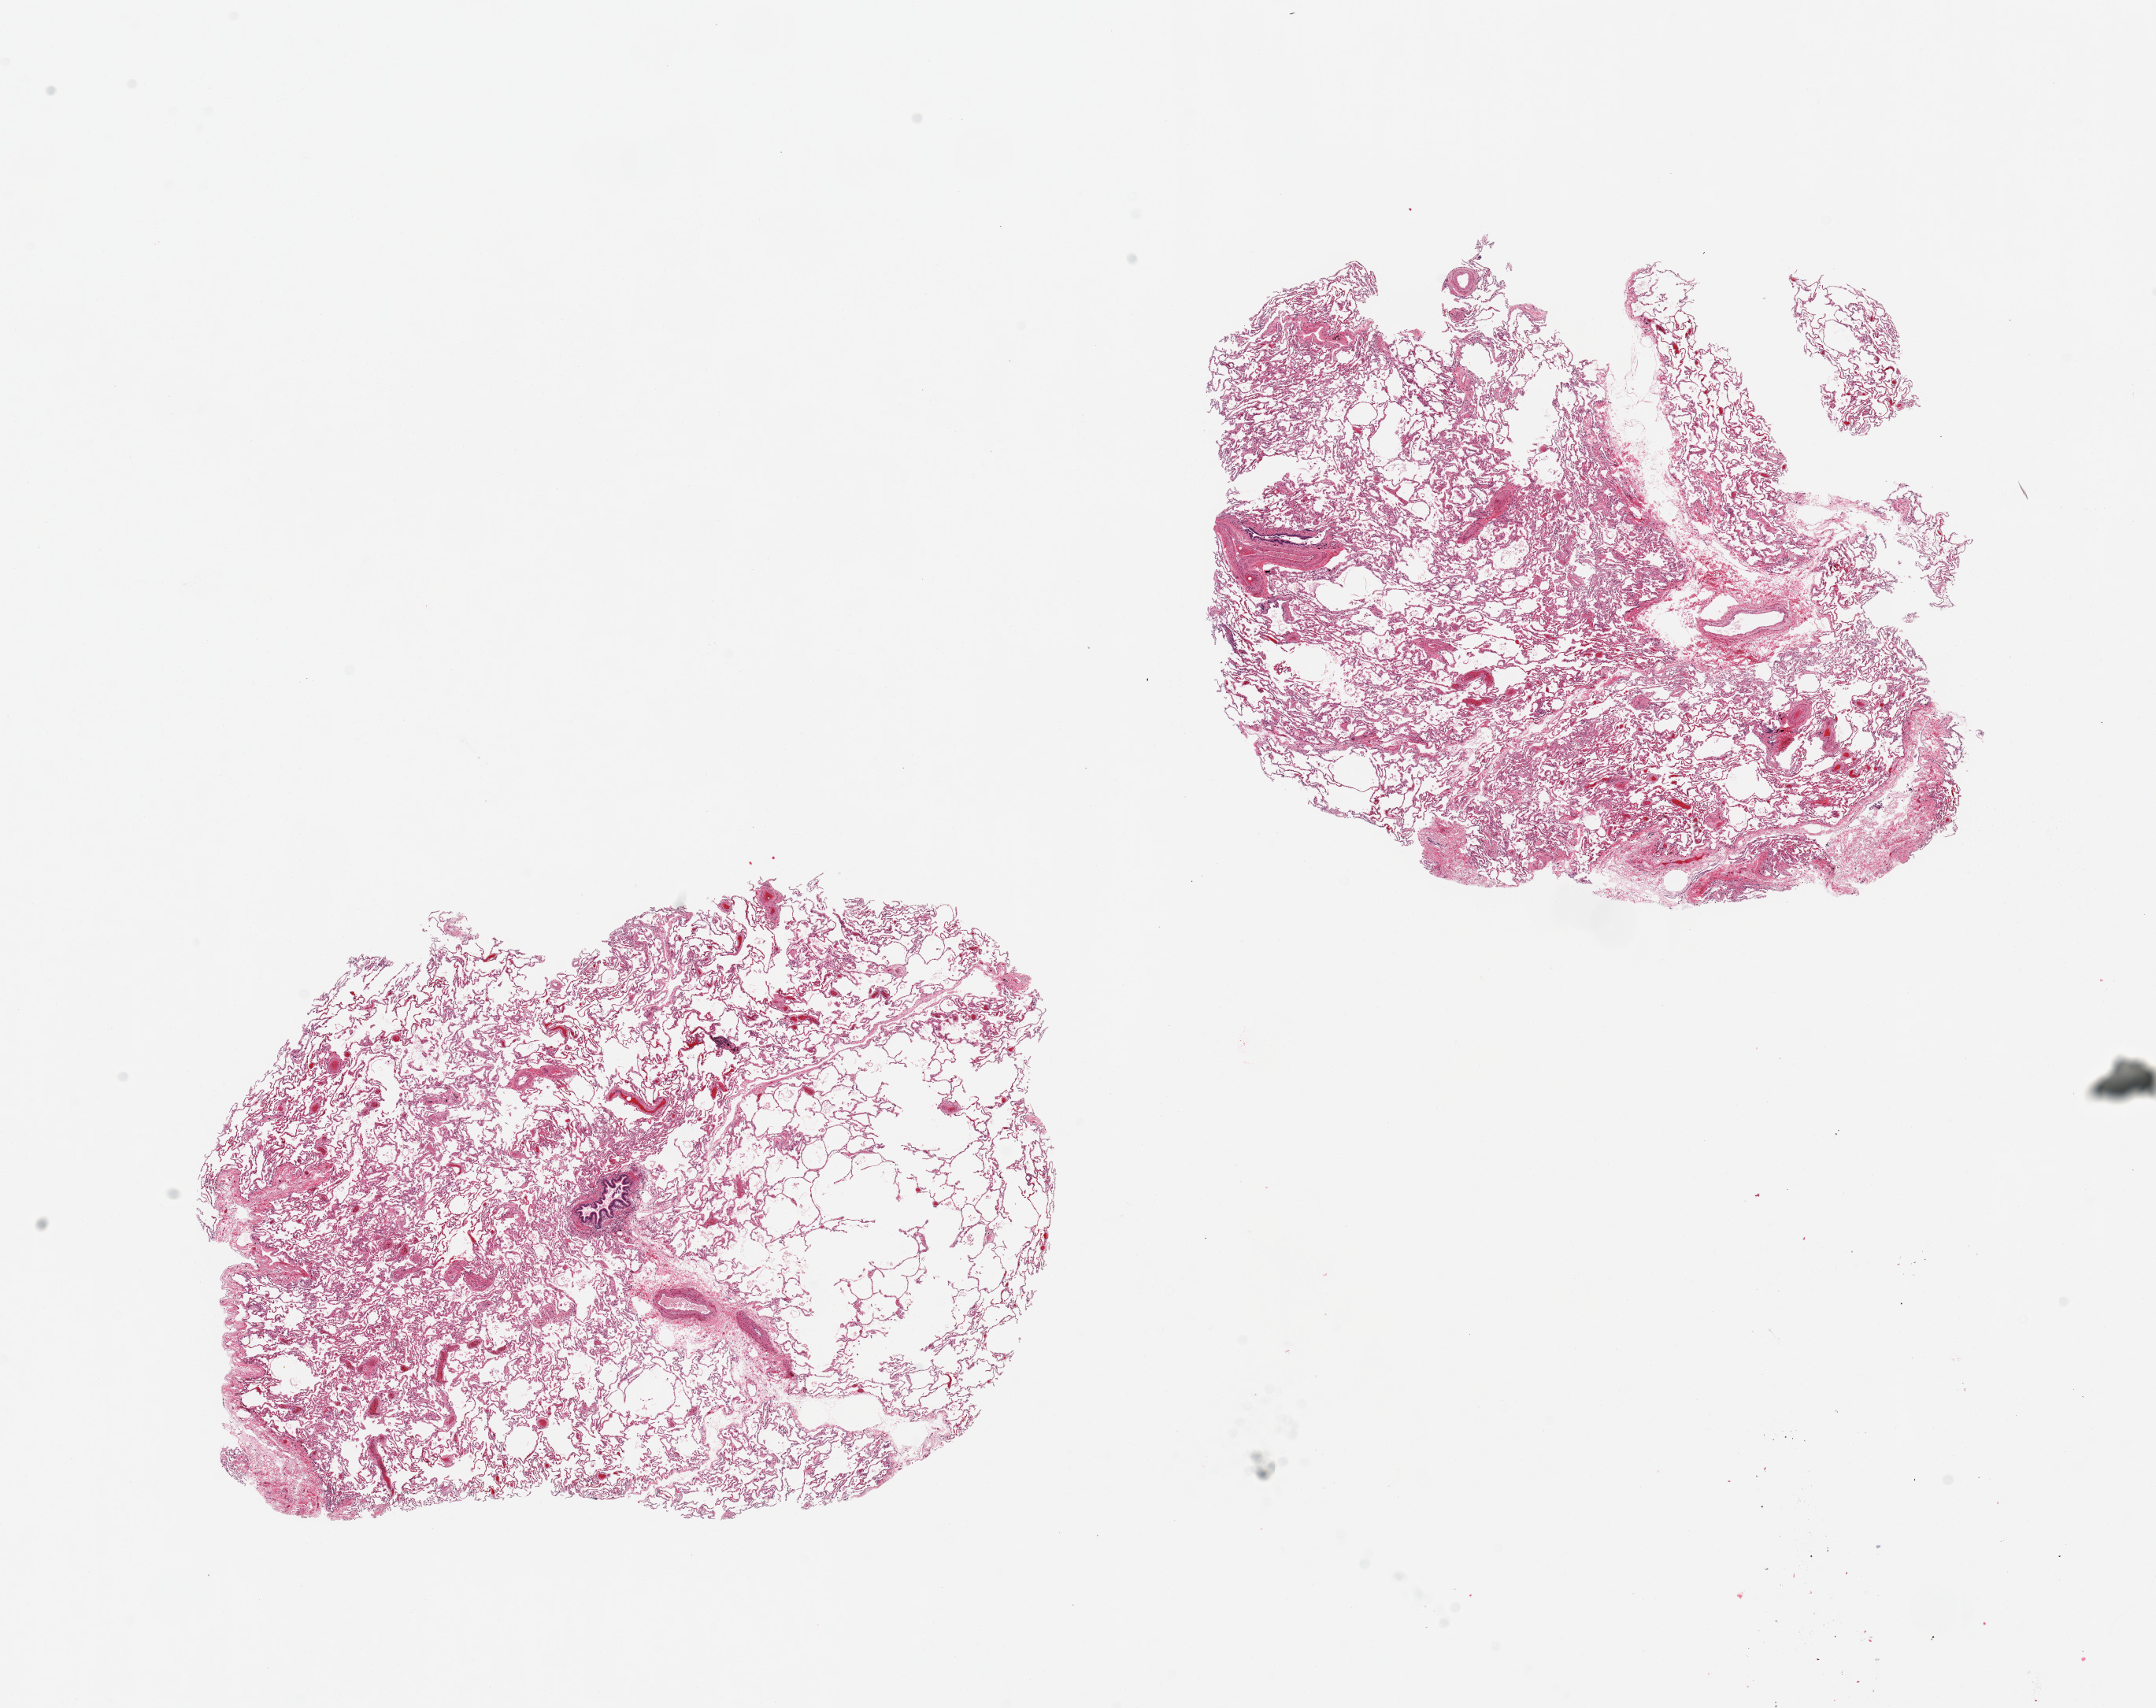
Whole-slide image, hematoxylin and eosin (H&E) stain, whole scanned area (about 21.7 x 17.2 mm, from a 20x scan) shown as a low-resolution overview. PAXgene-fixed paraffin-embedded (PFPE) section. Target tissue: lung. Donor tissue sample. Male donor.
Pathologist's review note for this sample: 2 pieces; congestion and large alveolar spaces bounded by thin and ruptured alveolar septa consistent with emphysema.